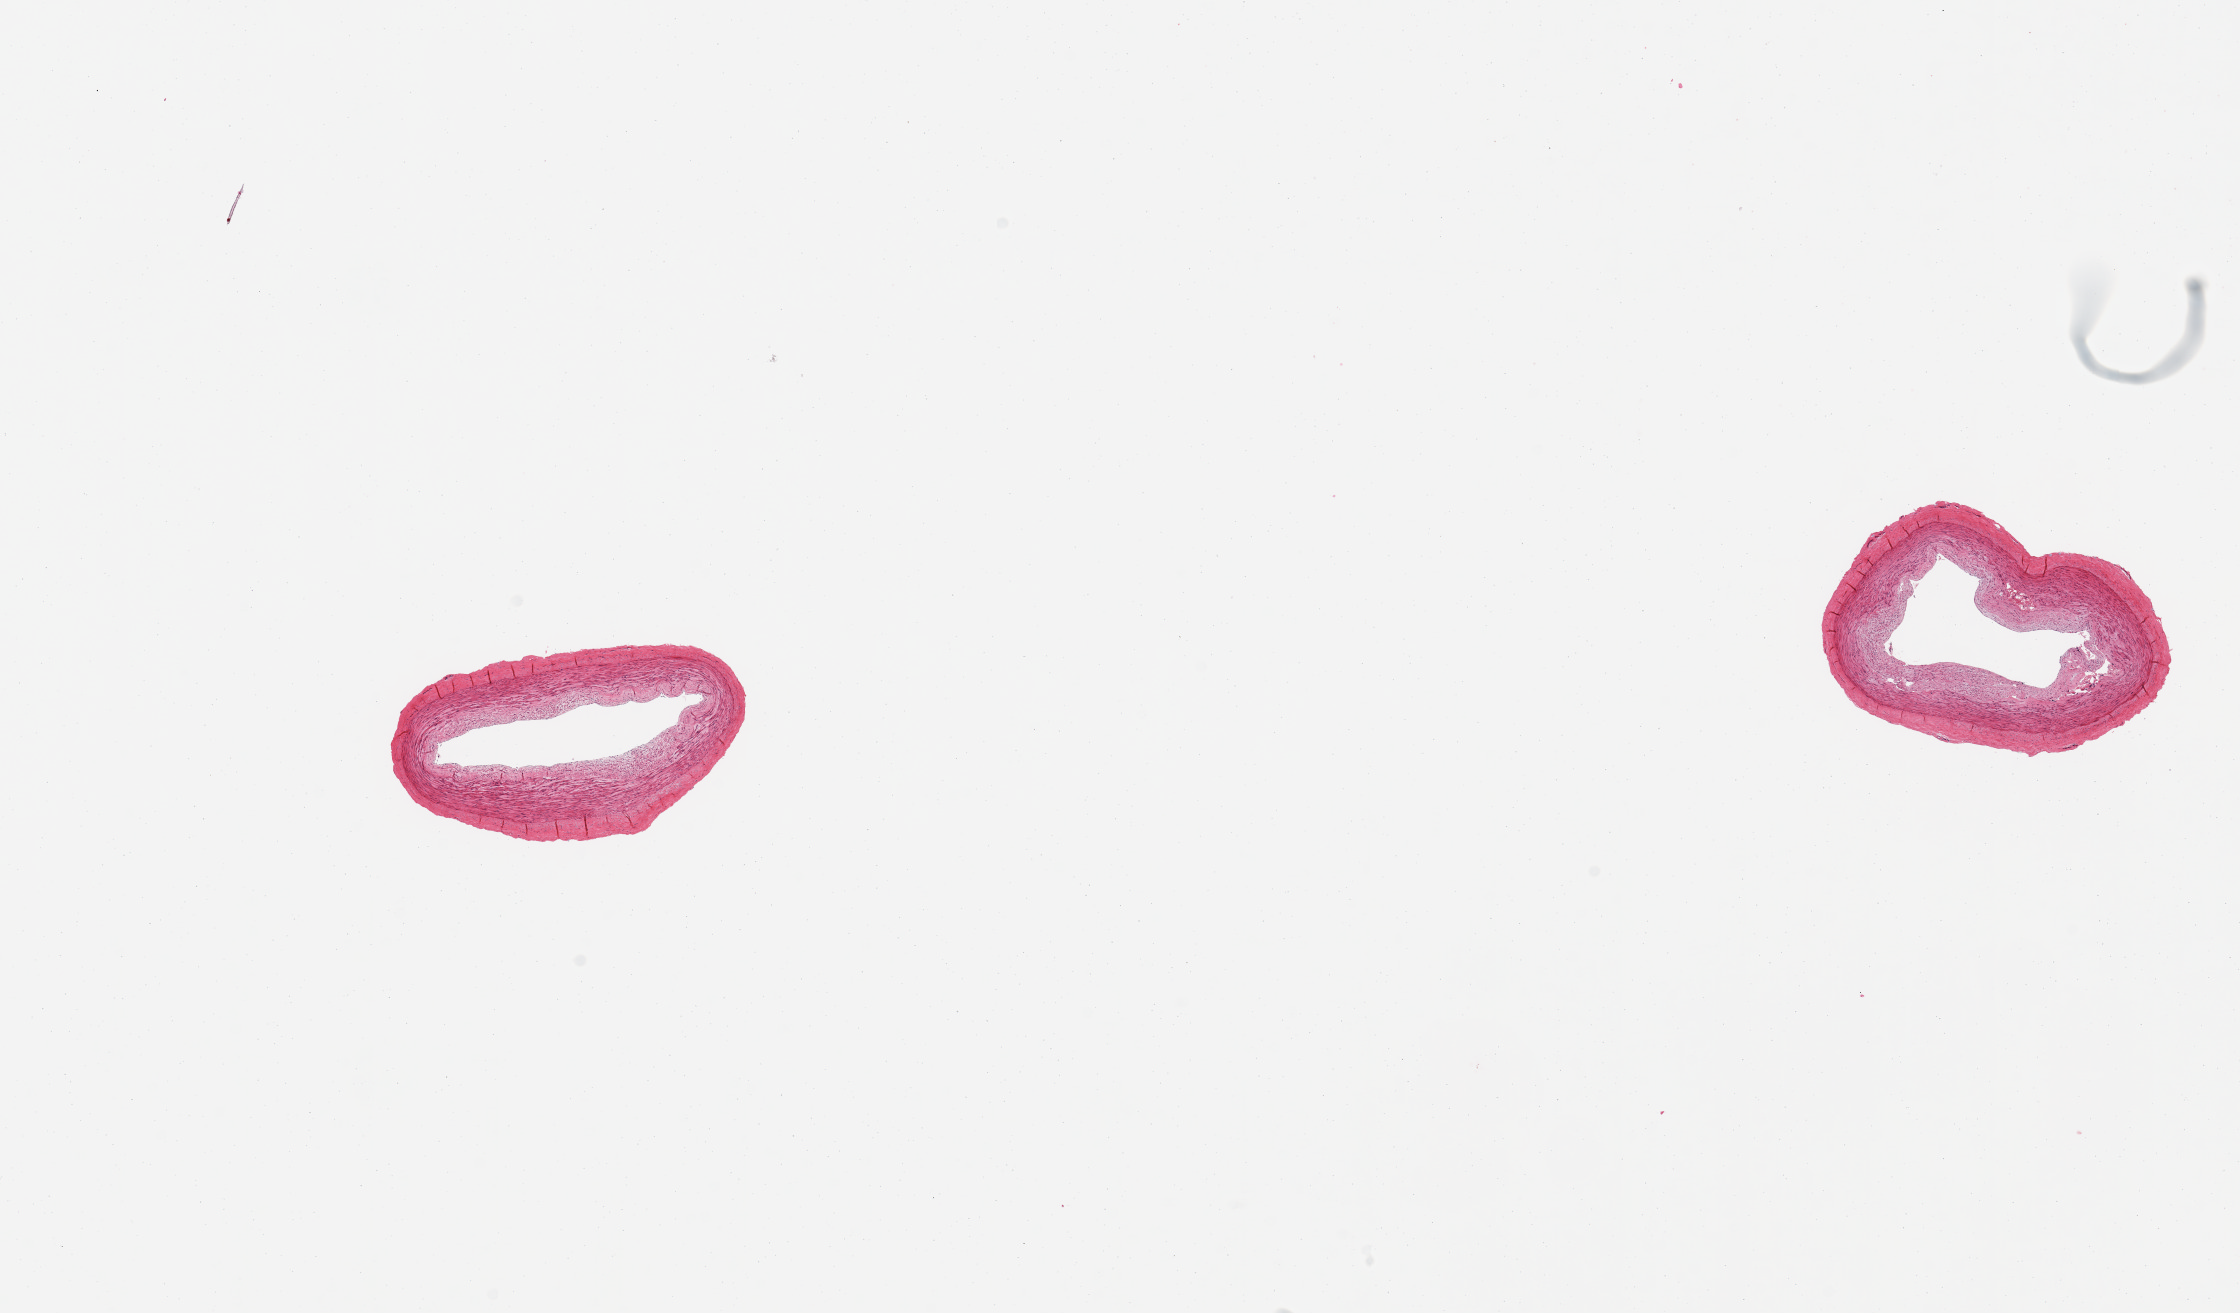
H&E whole-slide image, a low-resolution overview of the entire scanned area, about 17.7 x 10.4 mm, PAXgene-fixed paraffin-embedded (PFPE) section, target tissue: tibial artery, donor tissue sample. Donor sex: male.
Review note (as recorded): 2 pieces, no significant atherosis or adherent fat.